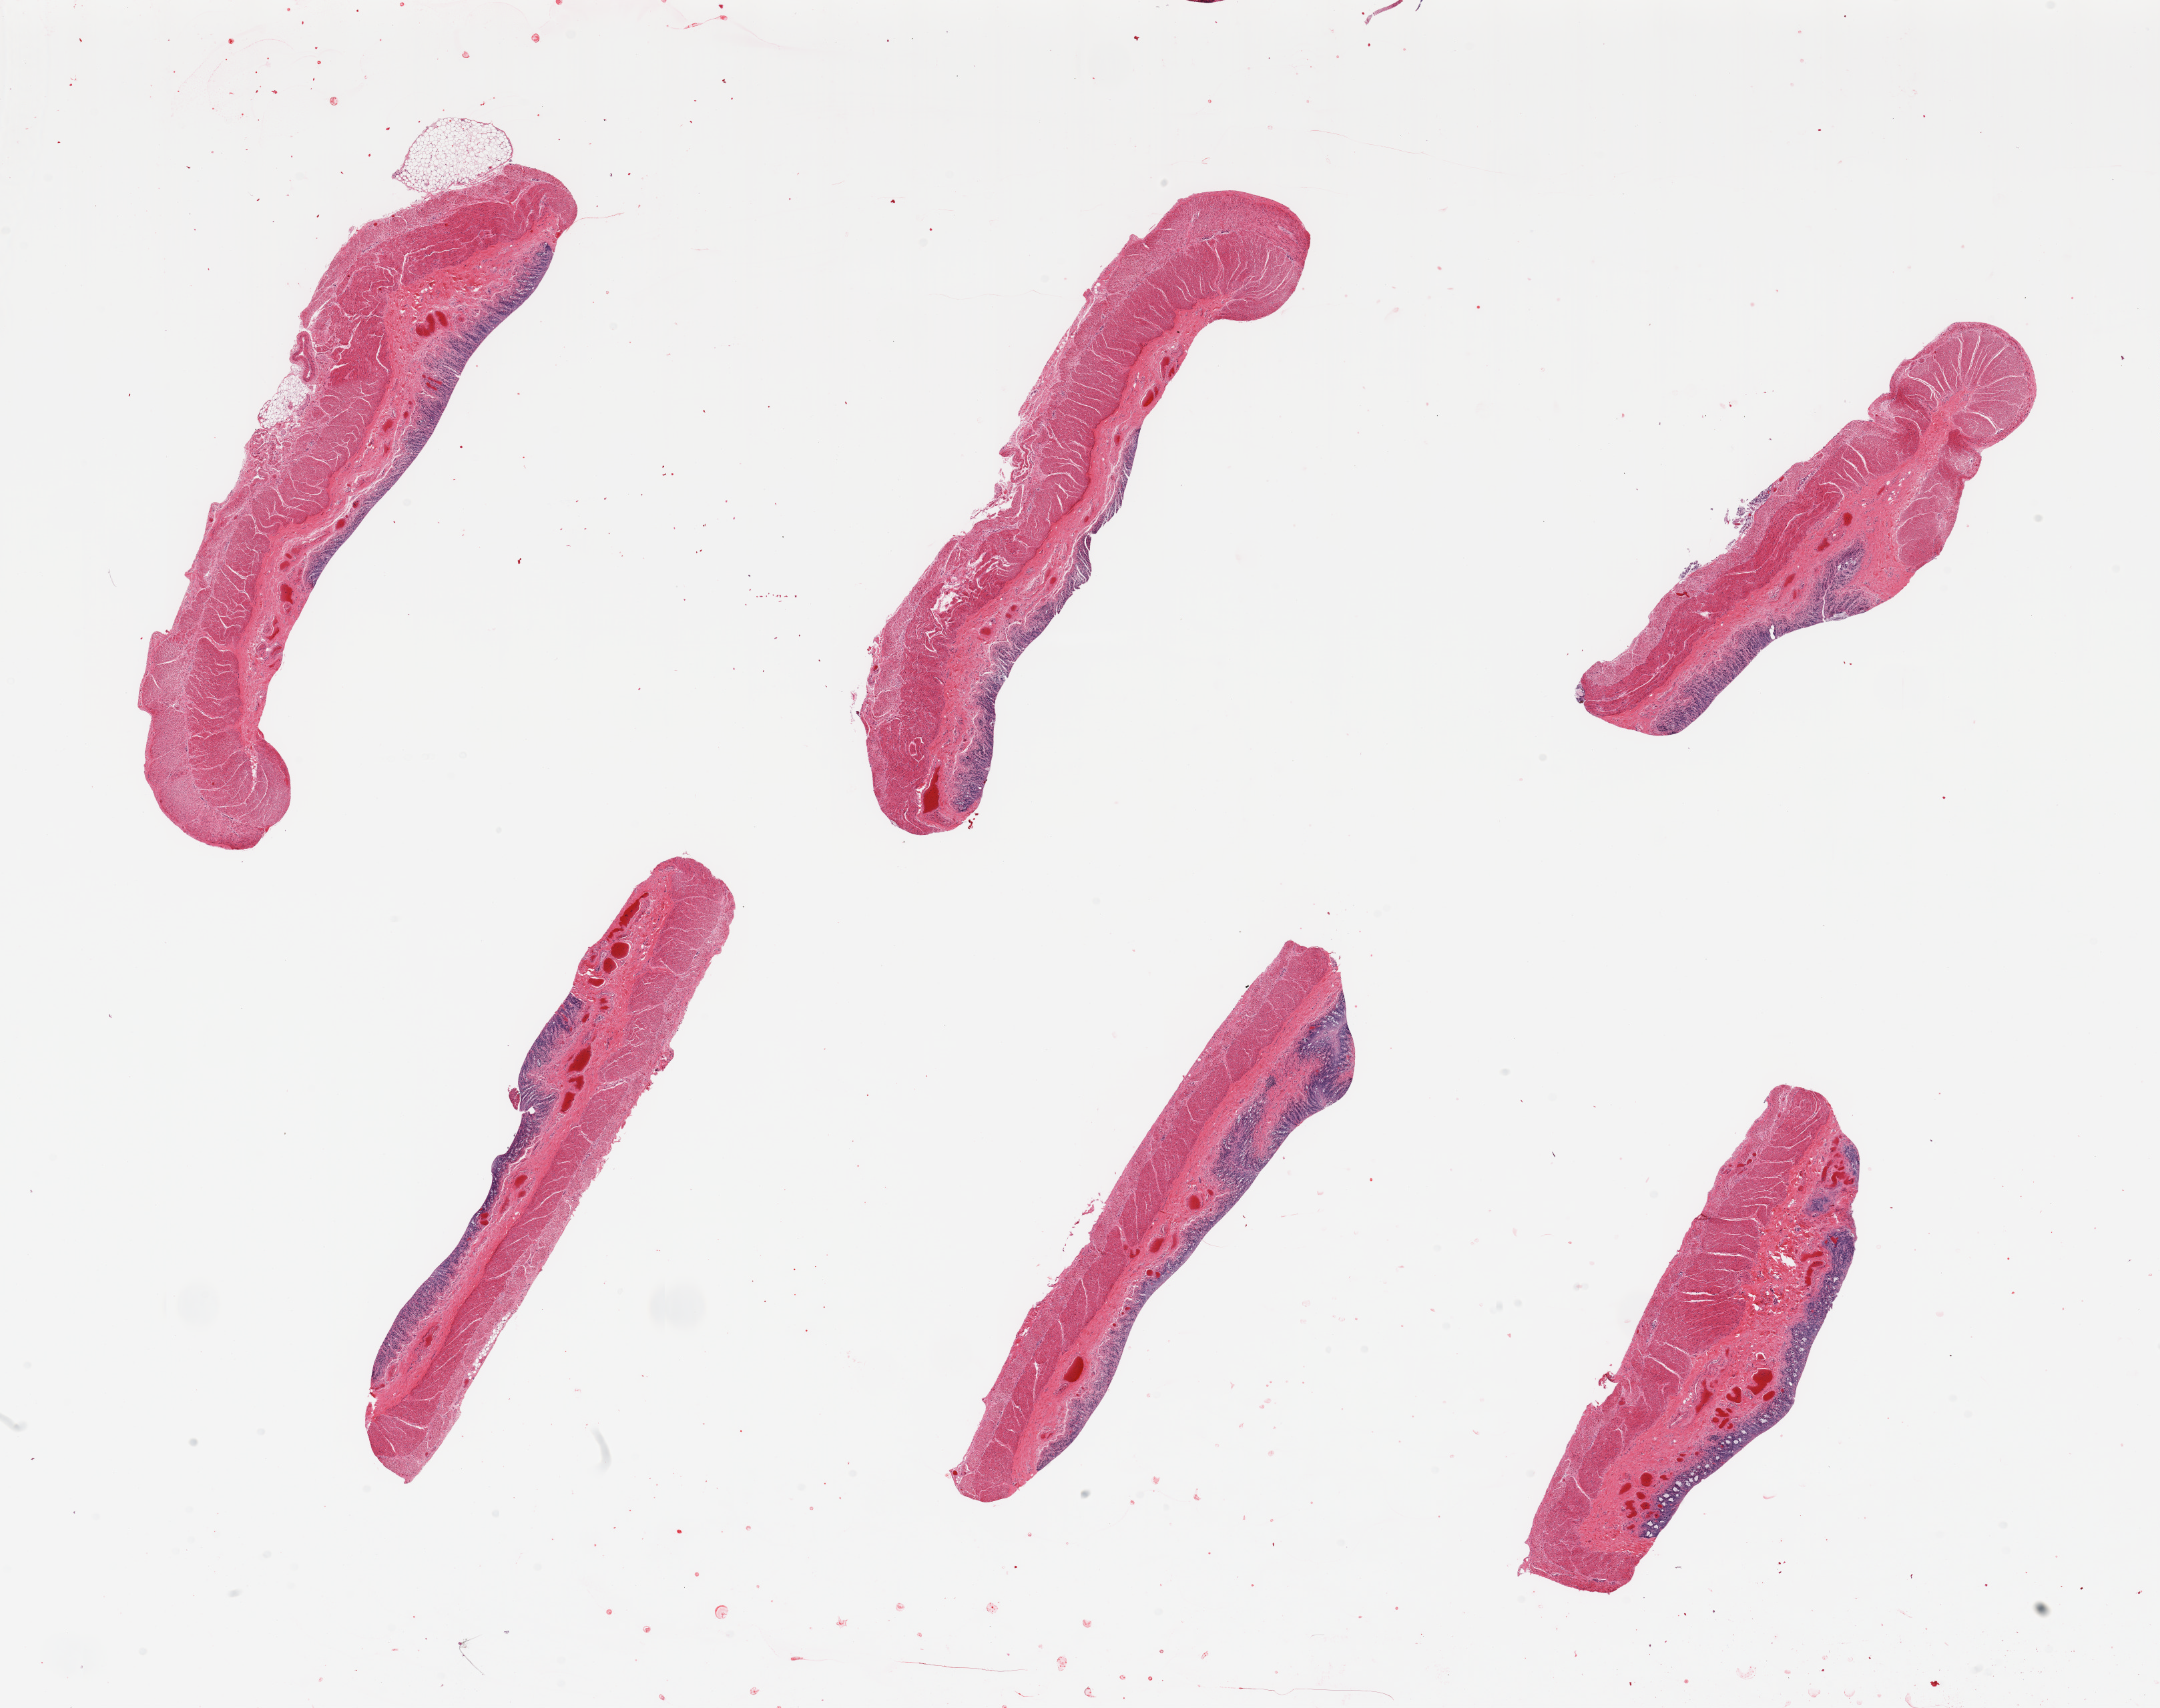
Haematoxylin and eosin whole-slide image — shown as a low-resolution overview of the whole scanned area (about 25.6 x 20.2 mm, slide scanned at 20x), PAXgene-fixed paraffin-embedded (PFPE) section, target tissue: transverse colon, donor tissue sample. Donor sex: female.
Review note (as recorded): 6 pieces; mucosa severely autolyzed; muscularis moderately autolyzed.